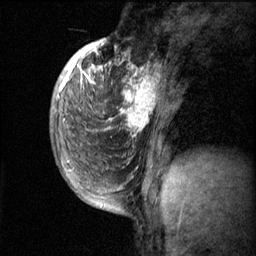
Breast MRI (dynamic contrast-enhanced), one sagittal slice. Position 18 of 60 along the scan axis. Dynamic contrast-enhanced series, image 2 of 3 at this slice position (ordered by acquisition). 1.5 T. TE 4.2 ms, TR 11.1 ms. 2 mm slice thickness. 256 × 256 image matrix, field of view 180 × 180 mm. Female patient, age 50 years.
Structures marked on this image (semi-automatic segmentation, software-assisted and operator-edited):
- analysis volume of interest (the breast-tissue region the enhancement analysis was run in; not a lesion): box from (x=82, y=56) to (x=168, y=143) px
- tumour enhancement mask (voxels above the 70 % enhancement threshold inside the analysis volume of interest): (x=82, y=64)–(x=160, y=133)